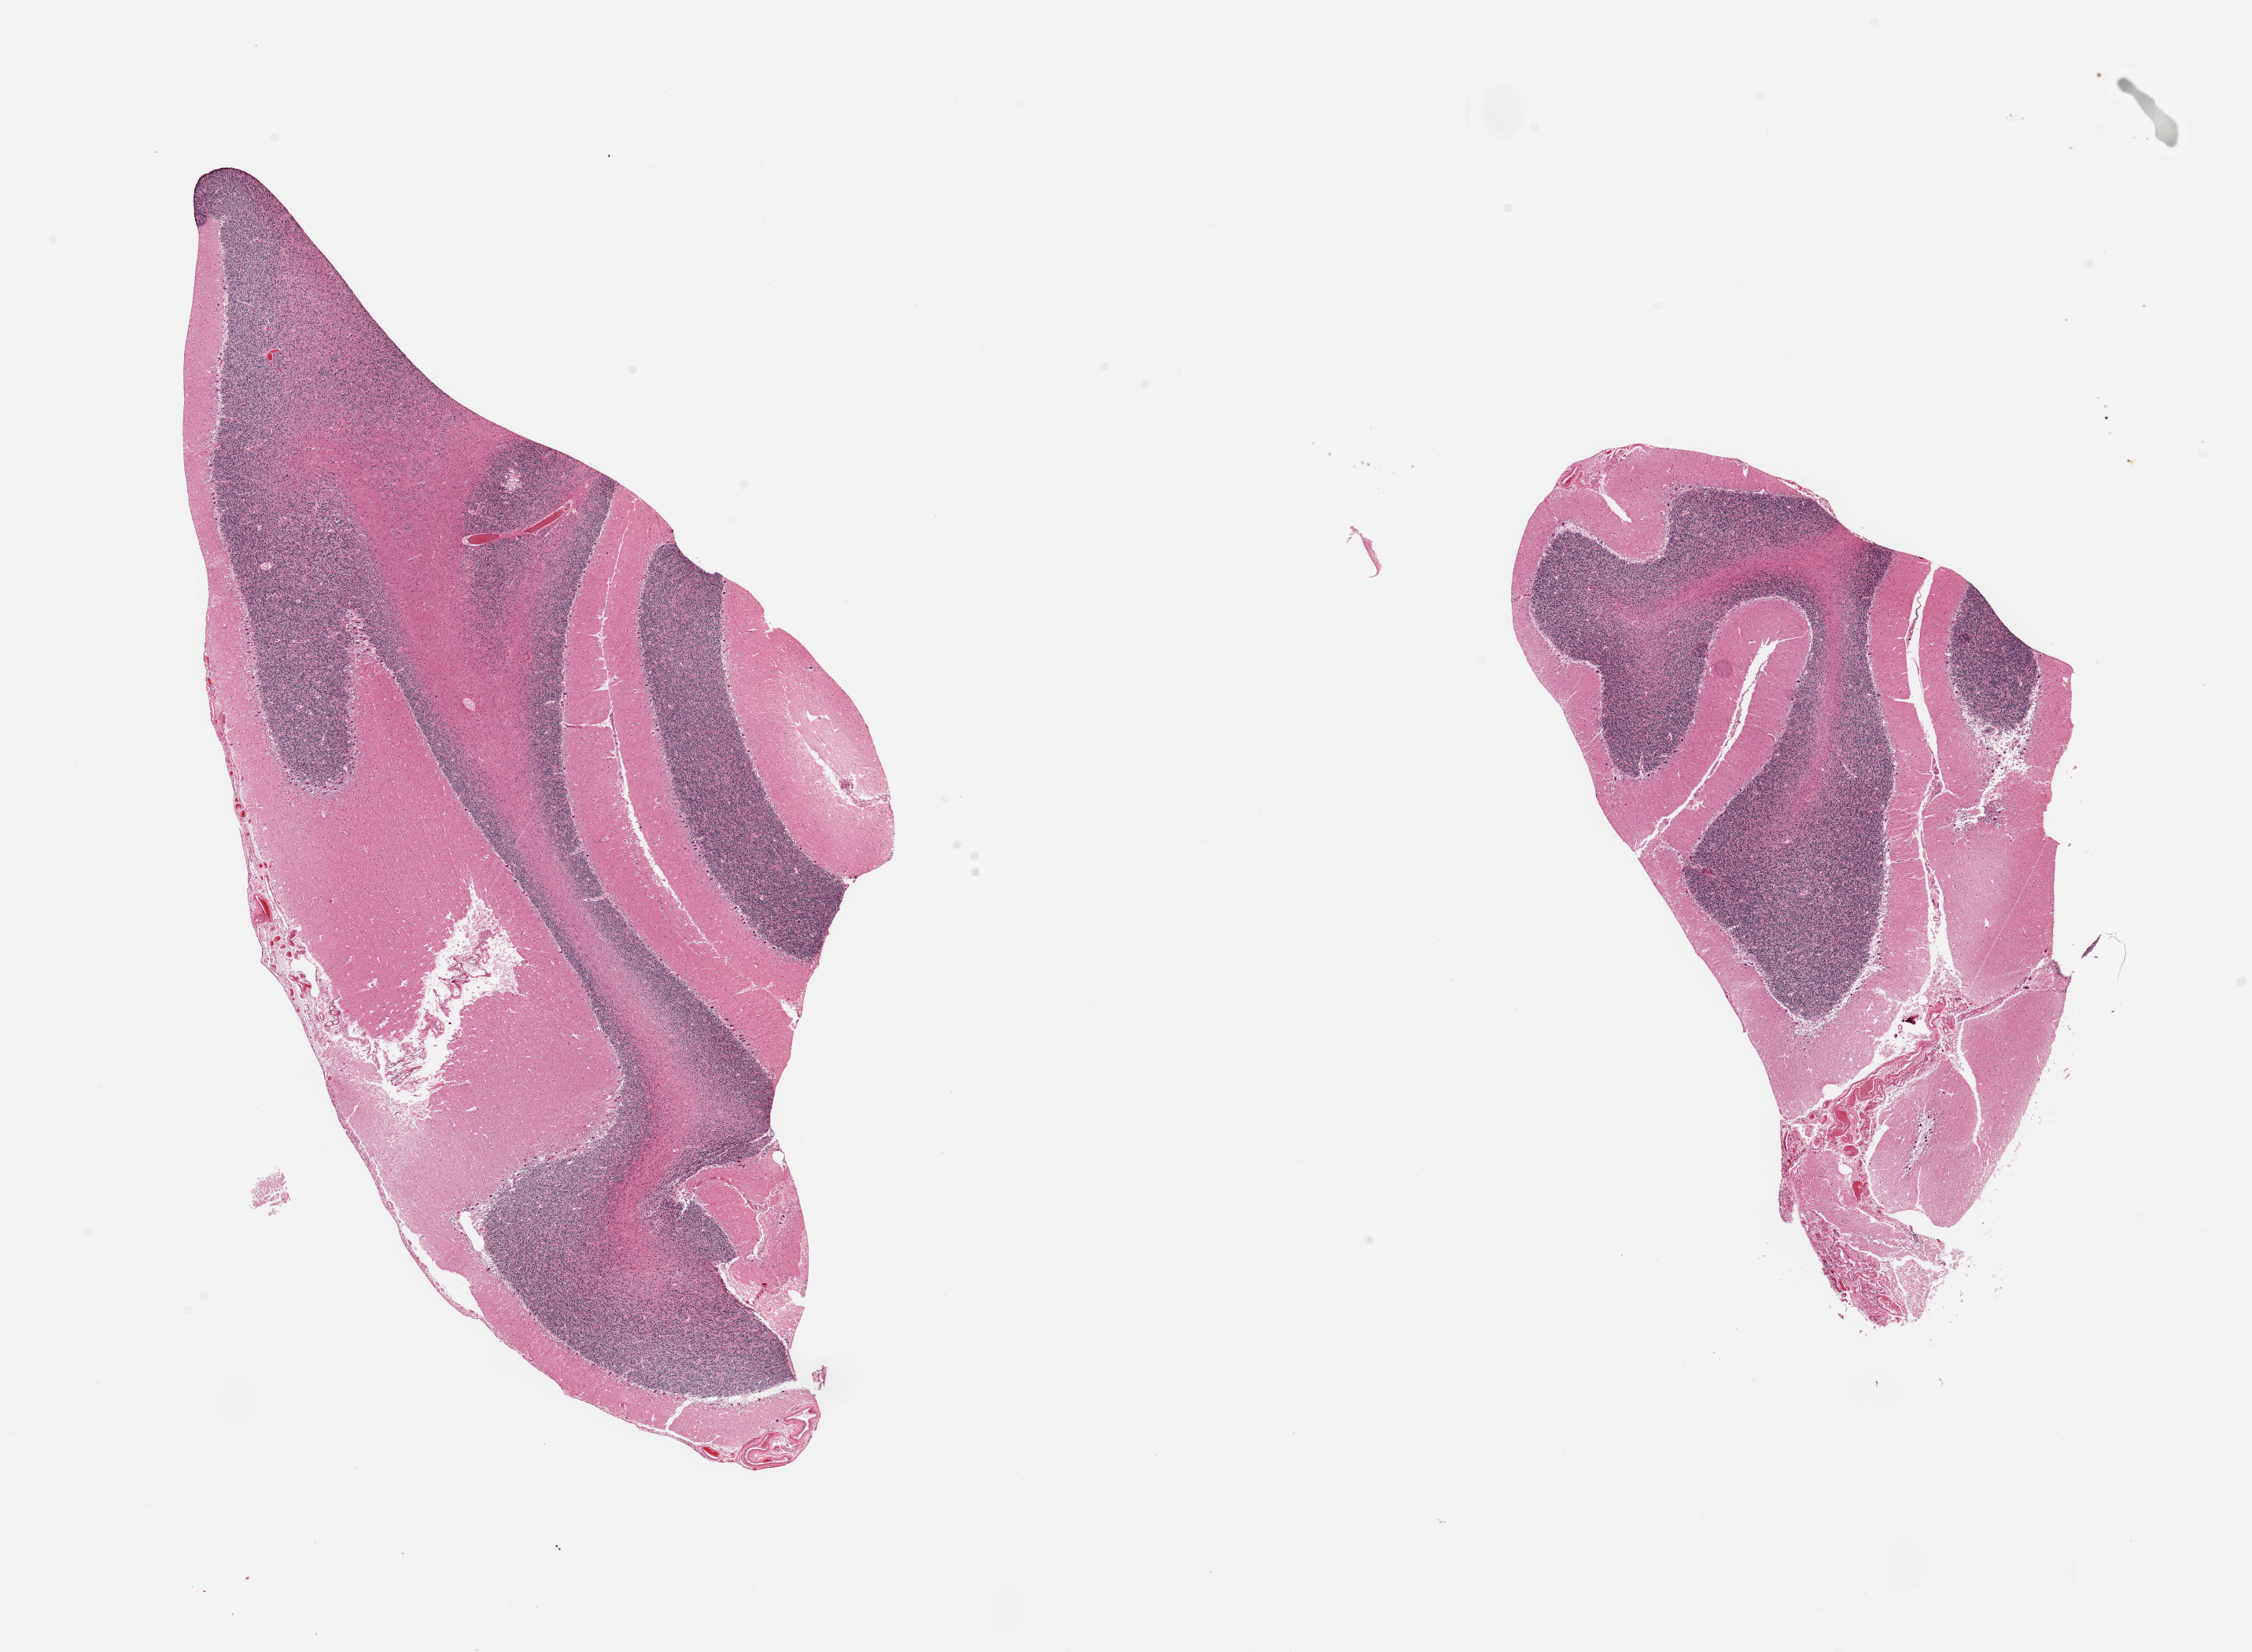
Hematoxylin and eosin (H&E) whole-slide image, whole scanned area (about 22.6 x 16.6 mm, slide scanned at 20x) shown as a low-resolution overview. PAXgene-fixed paraffin-embedded (PFPE) section. Sampled site (target tissue): cerebellum. Donor tissue sample. Female donor.
- pathologist's review note for this sample: 2 pieces